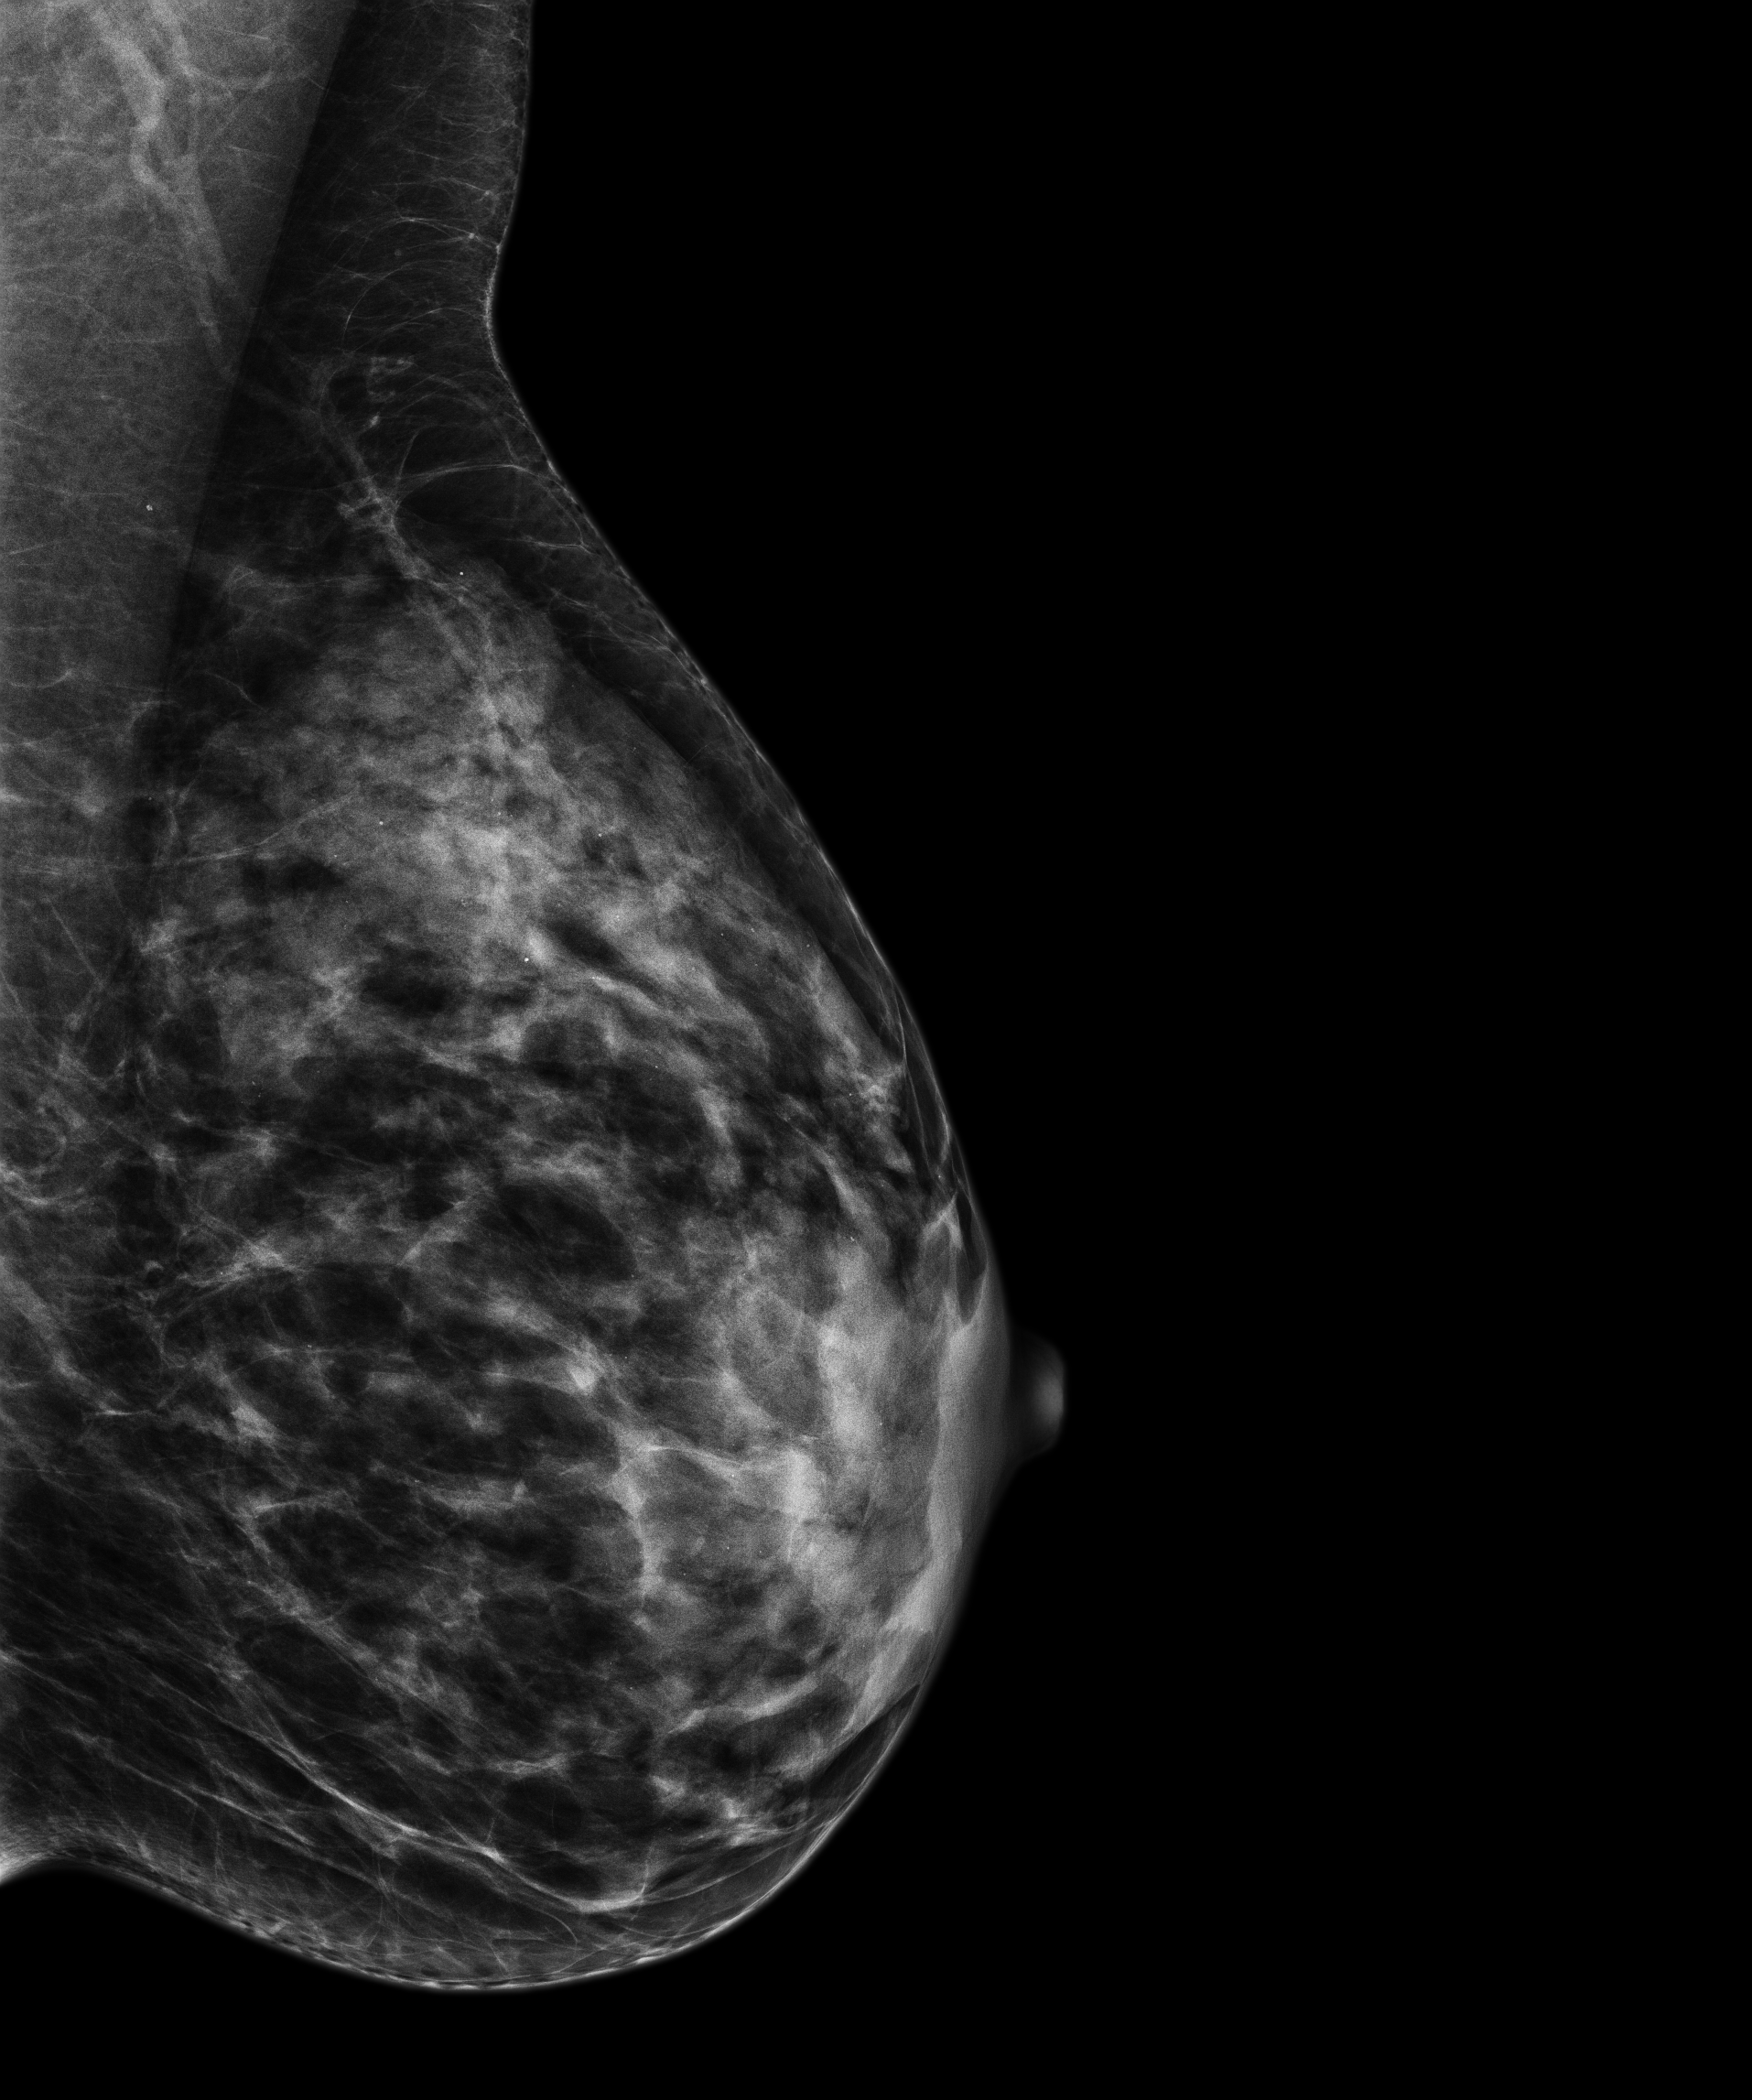
Diagnostic work-up study. Patient aged 47 years (female).
Image type: full-field digital mammogram. Breast: left. Projection: LM view.